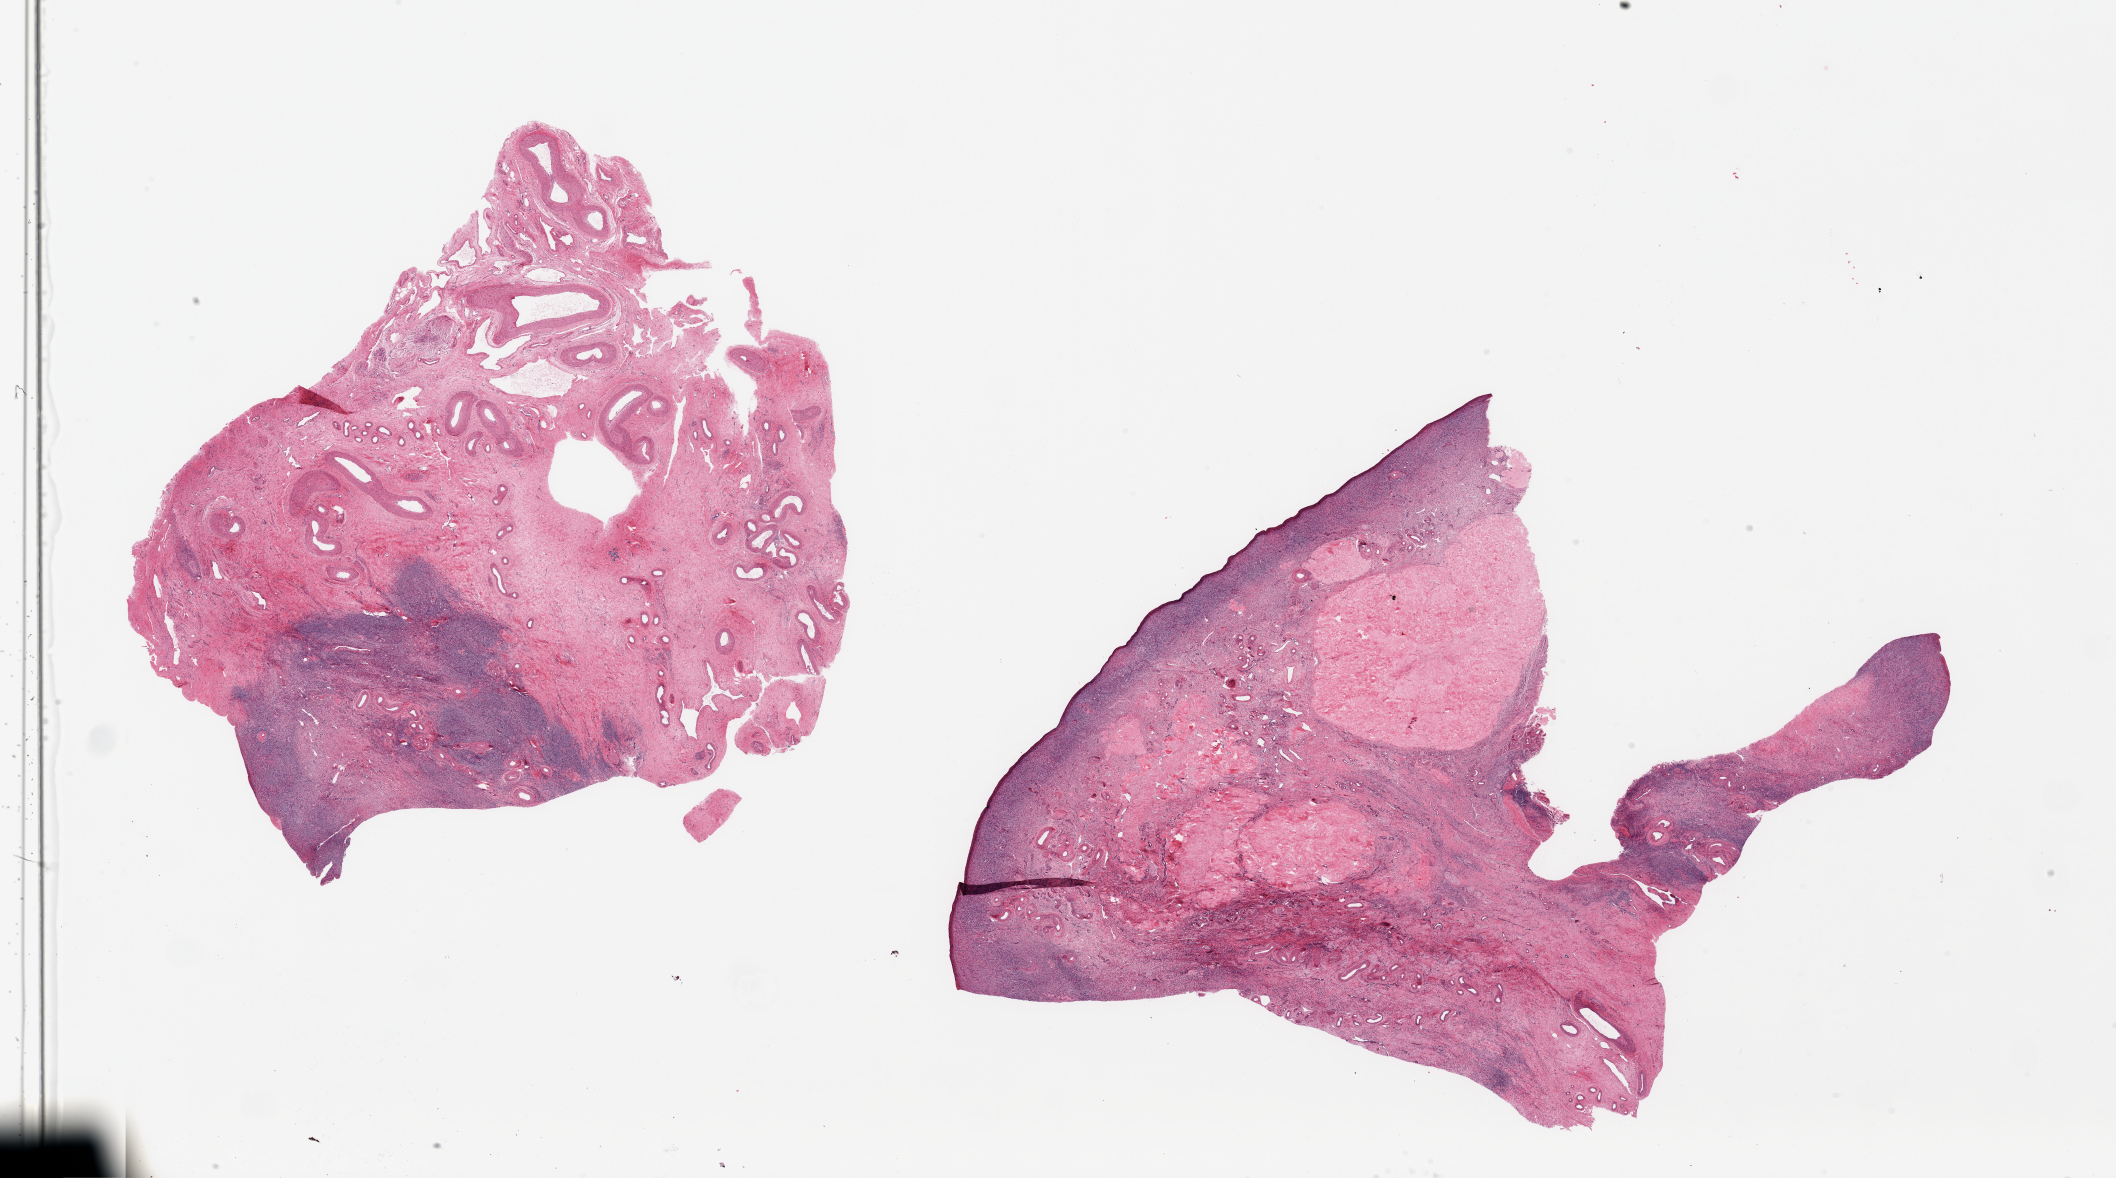
Digitized H&E-stained section, brightfield, a low-resolution overview of the entire scanned area, about 33.5 x 18.6 mm. PAXgene-fixed paraffin-embedded (PFPE) section. Target tissue: ovary. Donor tissue sample. Donor sex: female.
Review note (as recorded): 2 pieces; 1 piece is 70% vessels and fibrocollagenous stroma.